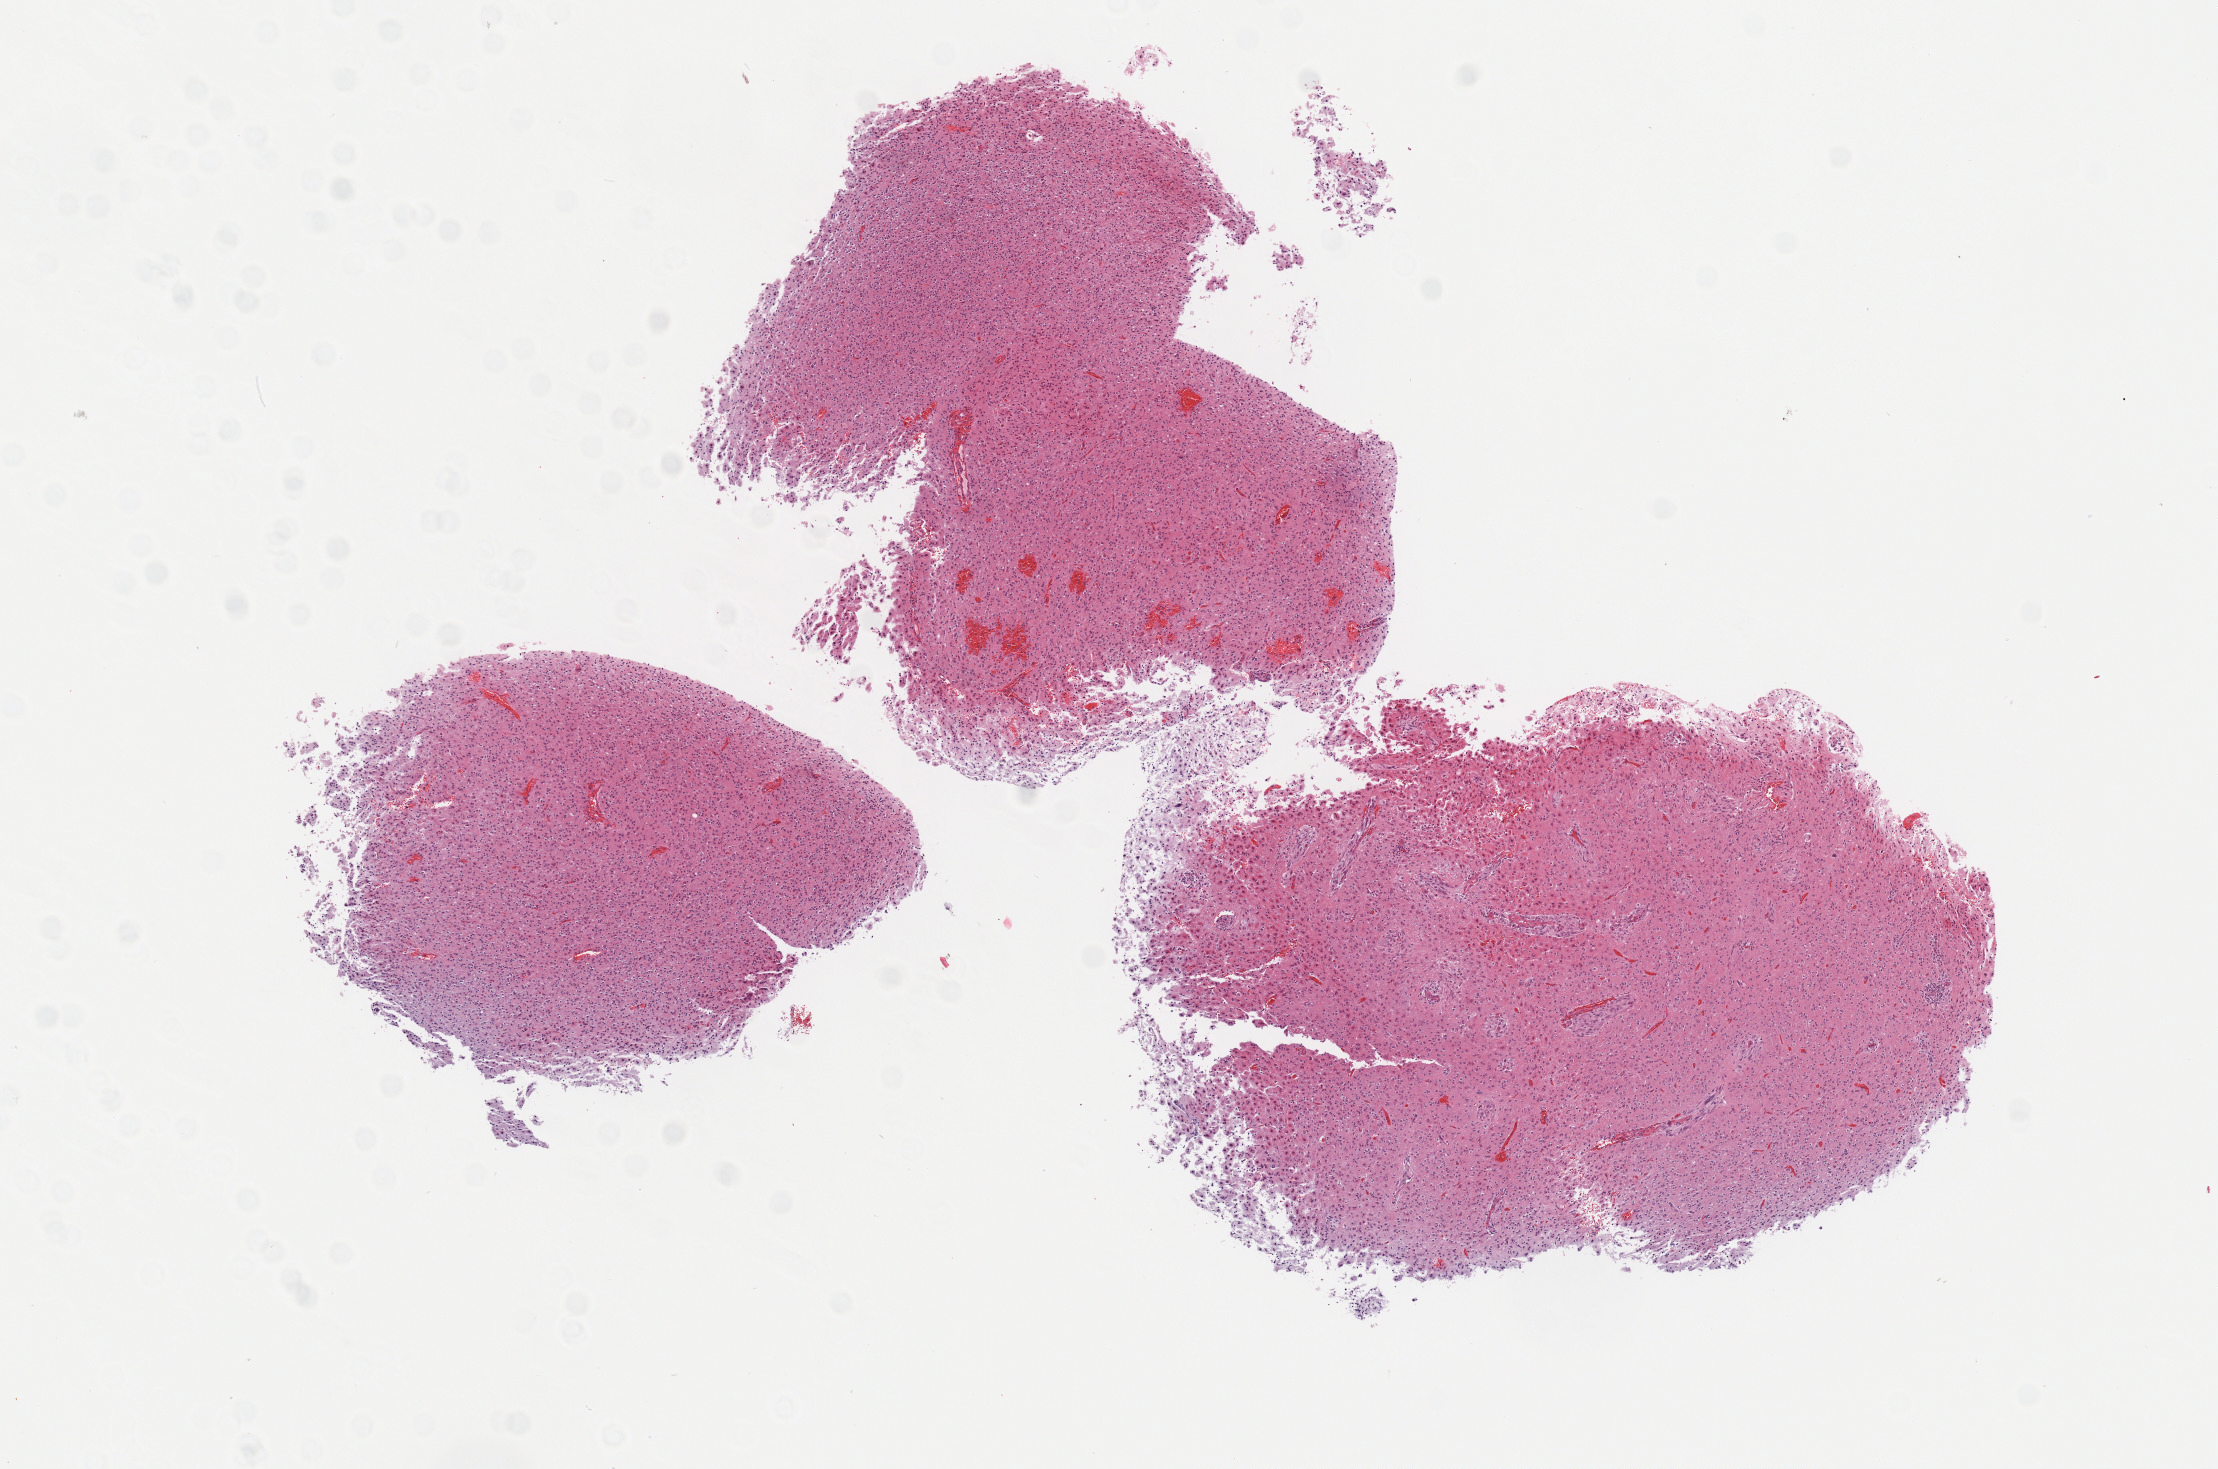
Digitized Hematoxylin and eosin (H&E) stained tissue section (whole slide), low-resolution overview of the scanned area, about 8.9 x 5.9 mm, formalin-fixed paraffin-embedded (FFPE) diagnostic section, primary tumour sample from the brain. Patient: female, age at initial diagnosis 63 years. Histologic grade: G3 (poorly differentiated).
* histologic diagnosis: Mixed glioma (cerebrum)